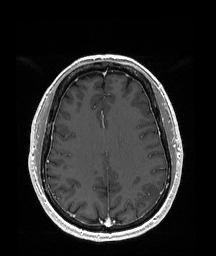
Brain MRI from a brain-tumour surgery series, one axial slice; position 74 of 192 along the scan axis; T1-weighted post-contrast; 216 × 256 image matrix, field of view 219 × 260 mm. From the clinical record (not read from this slice): histopathology: Glioblastoma; WHO grade: 4; IDH mutation: no; tumour location: Left Temporal Parietal.
Structures marked on this image (expert manual segmentation):
- tumour: box from (x=142, y=183) to (x=160, y=207) px